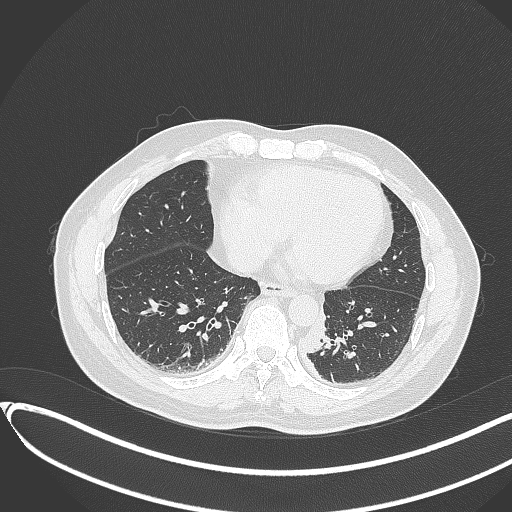
Chest CT, one axial slice; position 106 of 417 along the scan axis; reconstruction kernel B70f; lung window (W 1500 / L -600 HU); 1 mm slice thickness; 512 × 512 image matrix, field of view 400 × 400 mm. Male patient, age 54 years. From the clinical record (not read from this slice): clinical TNM (as recorded): T3 N0 M0.
Outlined on this slice (rectangle marked by the reading radiologist):
- lung tumour (recorded histology: squamous cell carcinoma): box from (x=303, y=304) to (x=331, y=355) px